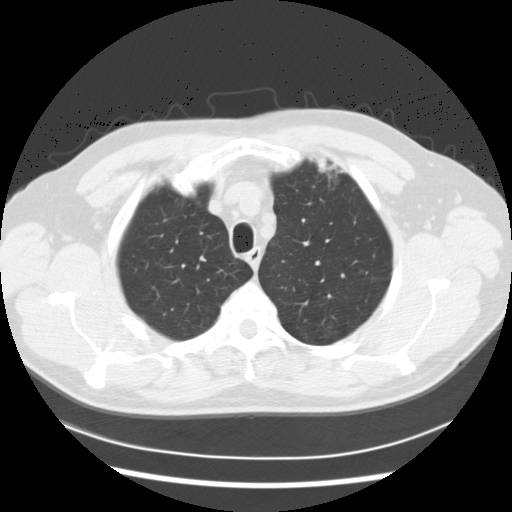
Axial slice from a low-dose chest CT screening exam, second screening round (one year after baseline), lung window (W 1500 / L -600 HU), 2.5 mm slice thickness, standard (soft-tissue) reconstruction kernel (STANDARD), 120 kVp, 512 × 512 image matrix, field of view 360 × 360 mm. Male participant, aged 56 years at enrolment. Former smoker at enrolment.
Expert reader's lesion annotation, bounding box (x1, y1, x2, y2) in pixels: (312, 157, 350, 198). No non-calcified nodule or mass ≥4 mm was recorded by the screening reader at this exam. Participant outcome: lung cancer diagnosed 486 days after this screen (after the third annual screen) — adenocarcinoma, NOS, left upper lobe, moderately differentiated (G2), stage IA (AJCC 6th edition), 15 mm at pathology.